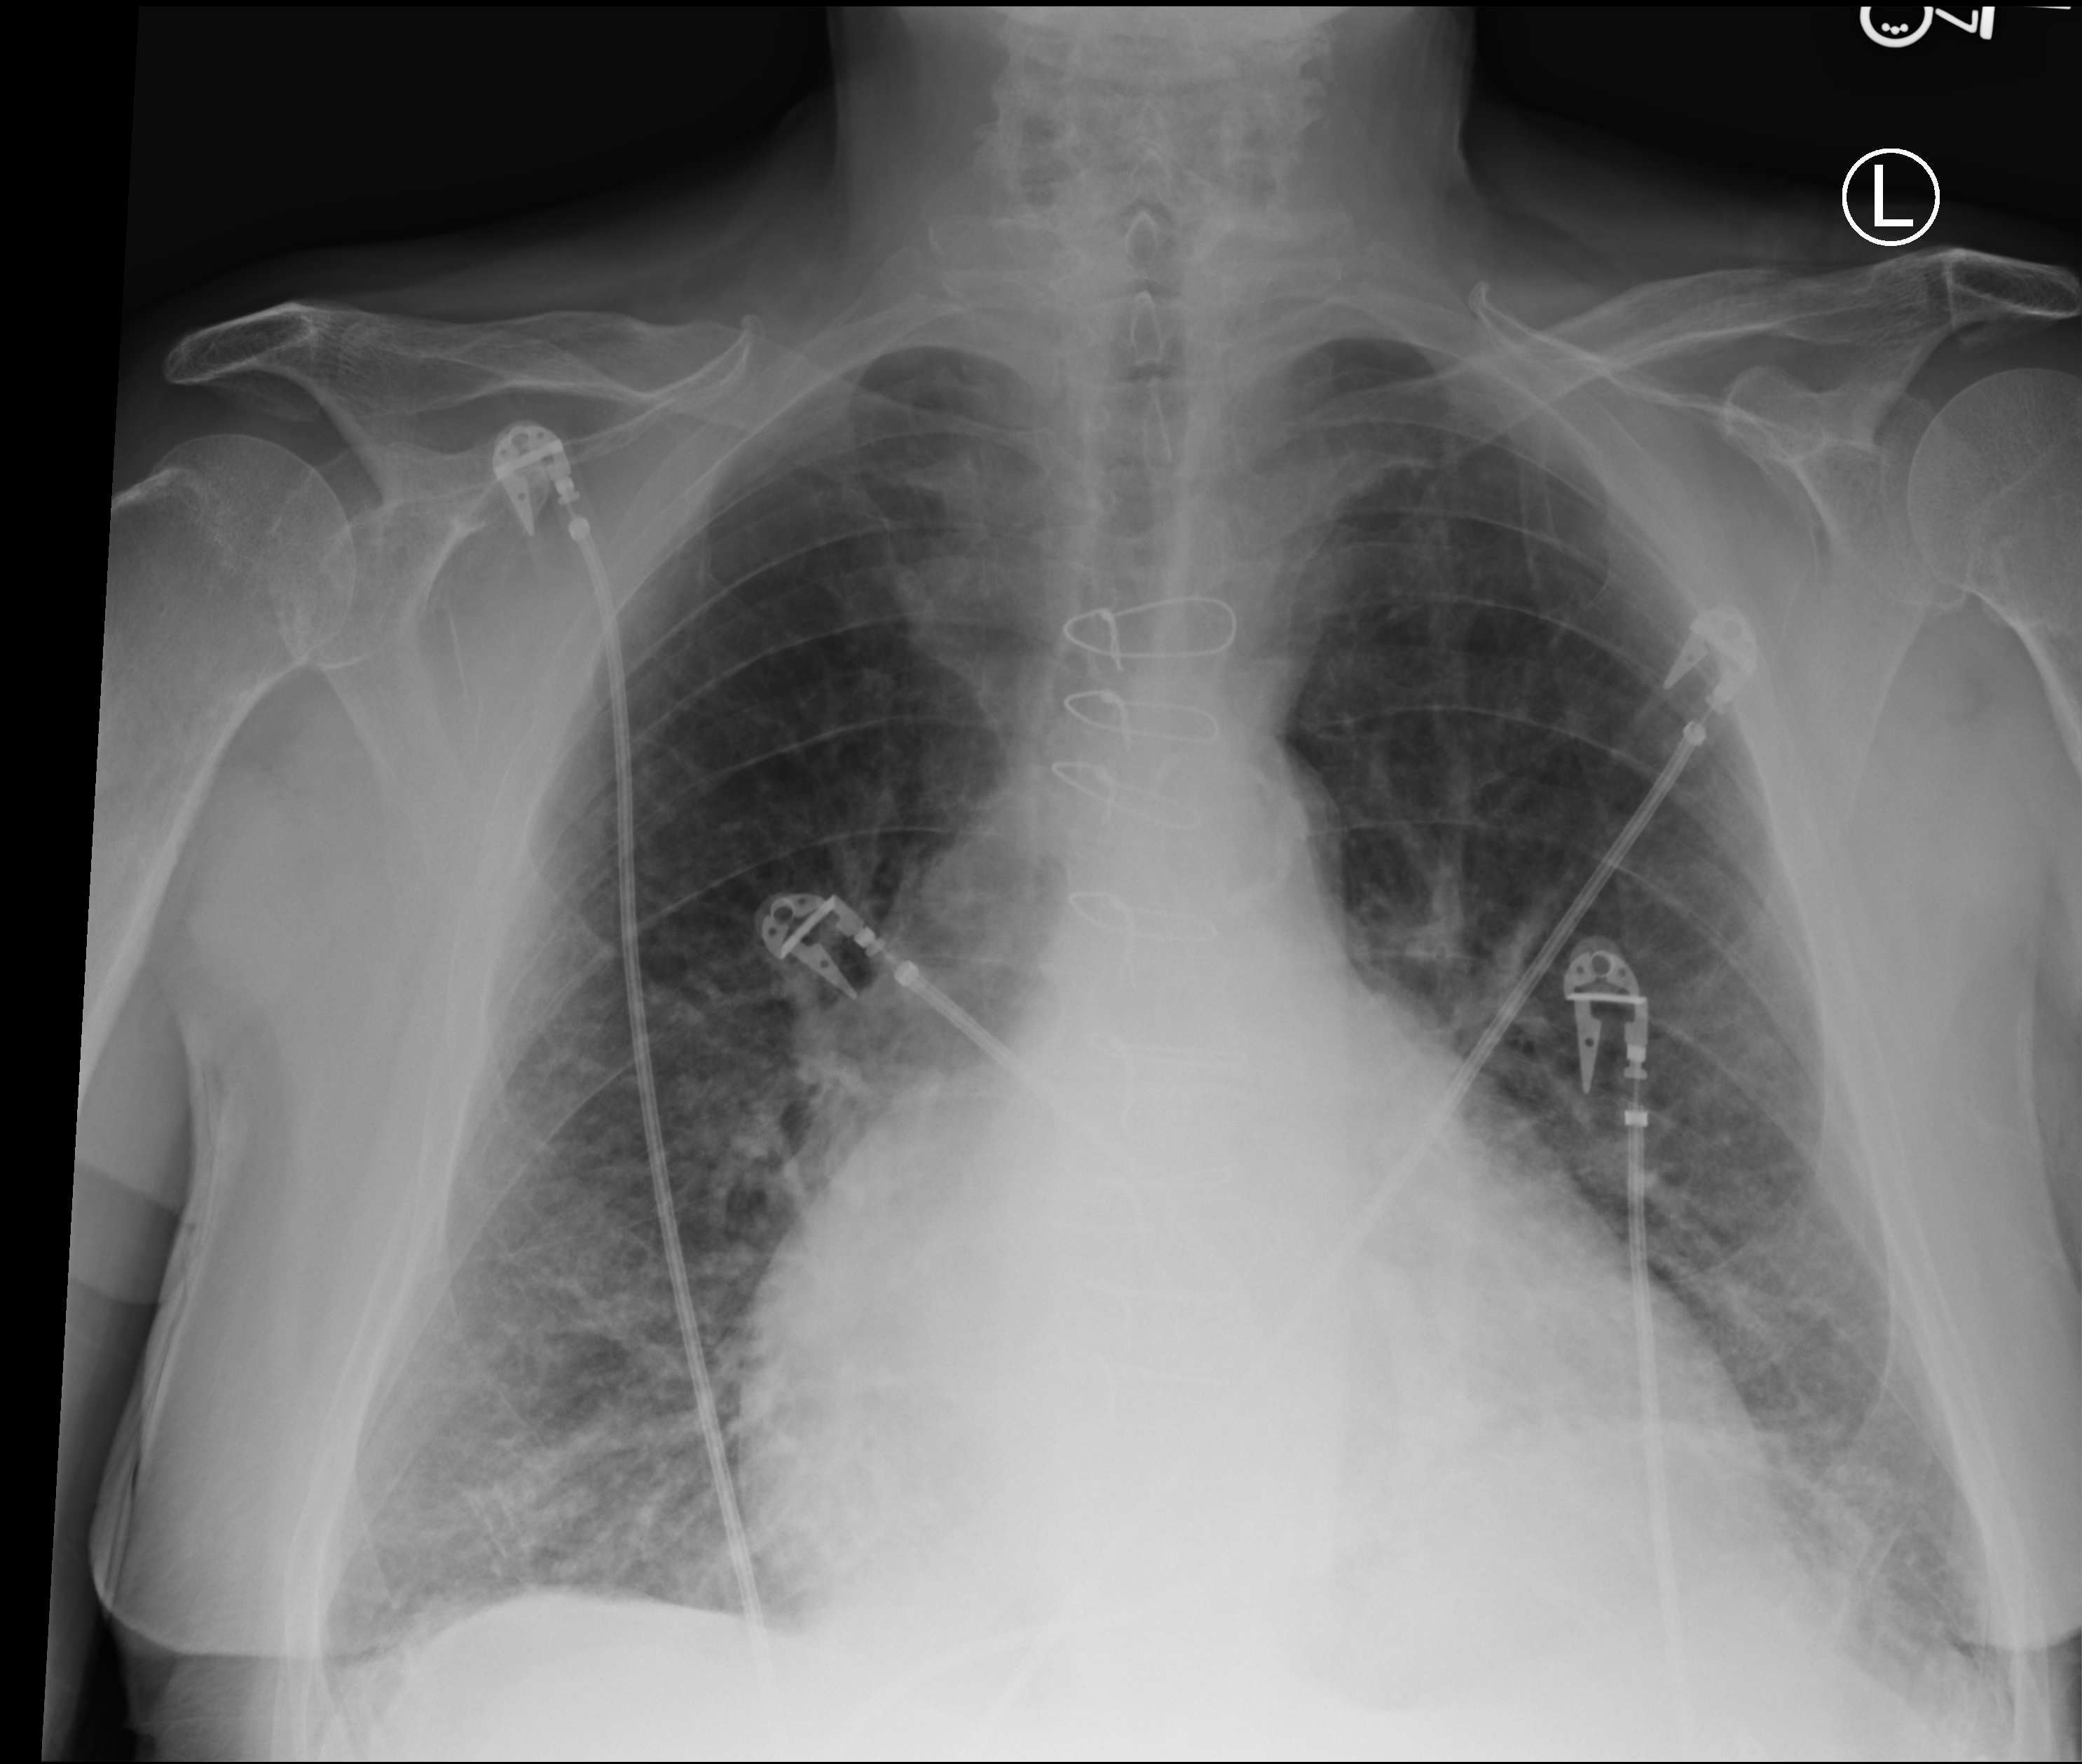
Portable chest radiograph; anteroposterior (AP) projection. Patient hospitalised with COVID-19; male, aged 75–90 years.
Admission-level facts for this patient (not findings on this image; timing relative to this image not recorded): mechanically ventilated during this hospital stay: yes.